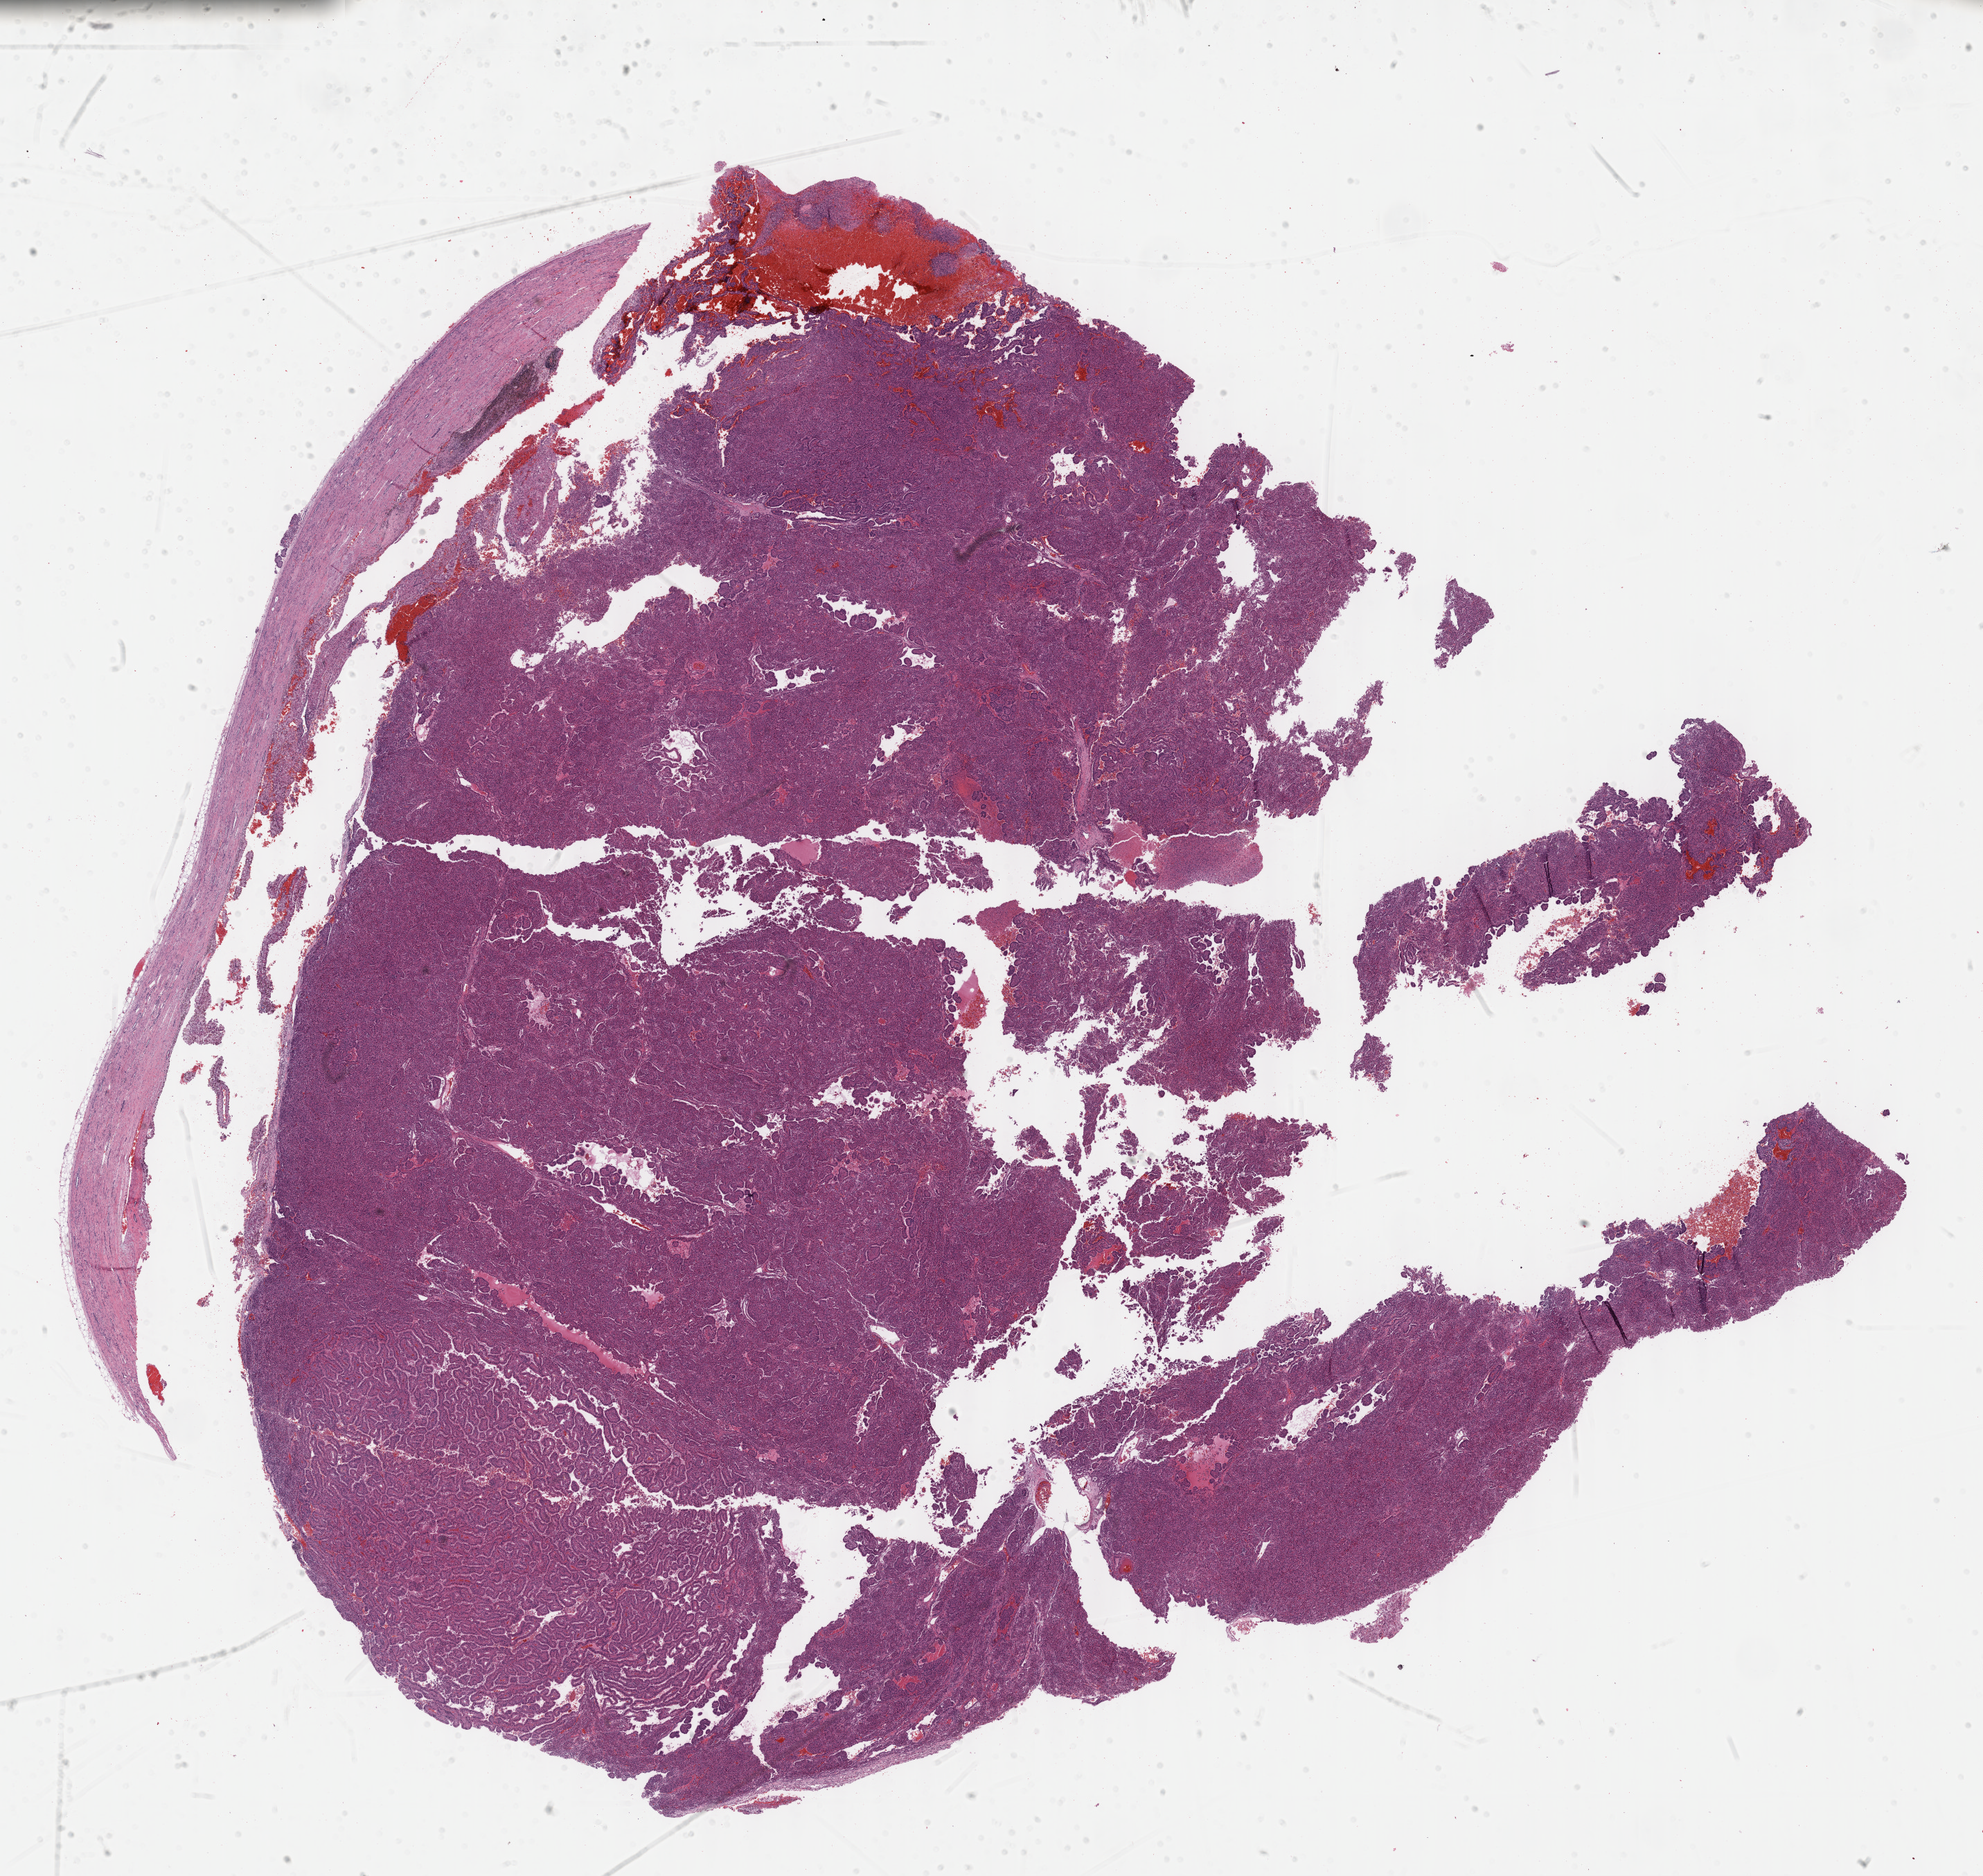
Whole-slide histology image, Hematoxylin and eosin (H&E) stained — a low-resolution overview of the entire scanned area, about 23.2 x 21.9 mm (from a 40x scan). FFPE section. Kidney, primary tumour sample. Female, age 63 years at initial diagnosis.
AJCC pathologic stage: II (7th edition). Pathologic diagnosis: Papillary adenocarcinoma, NOS.